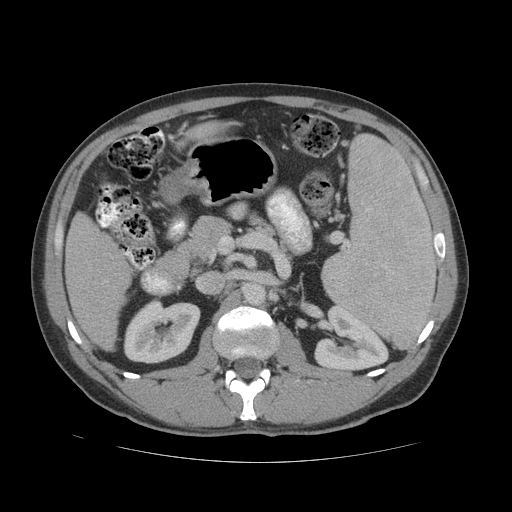
Contrast-enhanced abdominal CT (liver protocol), one axial slice. Slice 21 of 81 in the series (ordered by position). 140 kVp. Soft-tissue window (W 400 / L 40 HU). 512 × 512 image matrix. From the clinical record (not read from this slice): diagnosis: hepatocellular carcinoma (patient treated with transarterial chemoembolisation; whether this scan precedes or follows treatment is not stated here); TNM stage (as recorded): Stage-IVB; Child-Pugh class: B; tumour differentiation: well differentiated.
Annotated regions visible in this slice (semi-automatic segmentation, software-assisted and operator-edited):
- liver parenchyma outside the tumour (the mass and vessels are separate outlines, so this box may not span the whole liver): bounding box <66,212,132,350> (left, top, right, bottom; pixels)